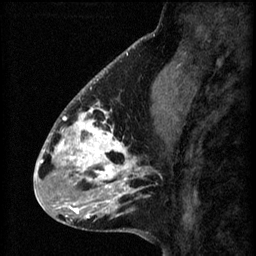
Breast MRI (dynamic contrast-enhanced), one sagittal slice. Position 21 of 60 along the scan axis. 3 images stored at this slice position (order not interpretable as contrast timing). 1.5 T. TE 4.2 ms, TR 8.2 ms. 256 × 256 image matrix, field of view 180 × 180 mm. Female patient, age 41 years.
Structures marked on this image (semi-automatically segmented with operator editing):
- analysis volume of interest (the breast-tissue region the enhancement analysis was run in; not a lesion): box from (x=56, y=104) to (x=157, y=207) px
- tumour enhancement mask (voxels above the 70 % enhancement threshold inside the analysis volume of interest): (x=56, y=104)–(x=144, y=207)